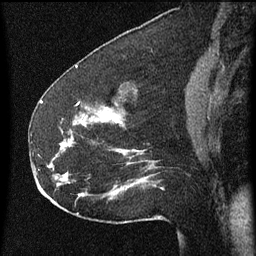
Breast MRI (dynamic contrast-enhanced), one sagittal slice. Slice 27 of 60 in the series (ordered by position). Dynamic contrast-enhanced series, image 2 of 3 at this slice position (ordered by acquisition). 1.5 T. TE 4.2 ms, TR 8 ms. 2 mm slice thickness. 256 × 256 image matrix, field of view 180 × 180 mm. Female patient, age 52 years.
Structures marked on this image (semi-automatically segmented with operator editing):
- analysis volume of interest (the breast-tissue region the enhancement analysis was run in; not a lesion): bounding box <54,110,163,207> (left, top, right, bottom; pixels)
- tumour enhancement mask (voxels above the 70 % enhancement threshold inside the analysis volume of interest): <61,114,163,191>